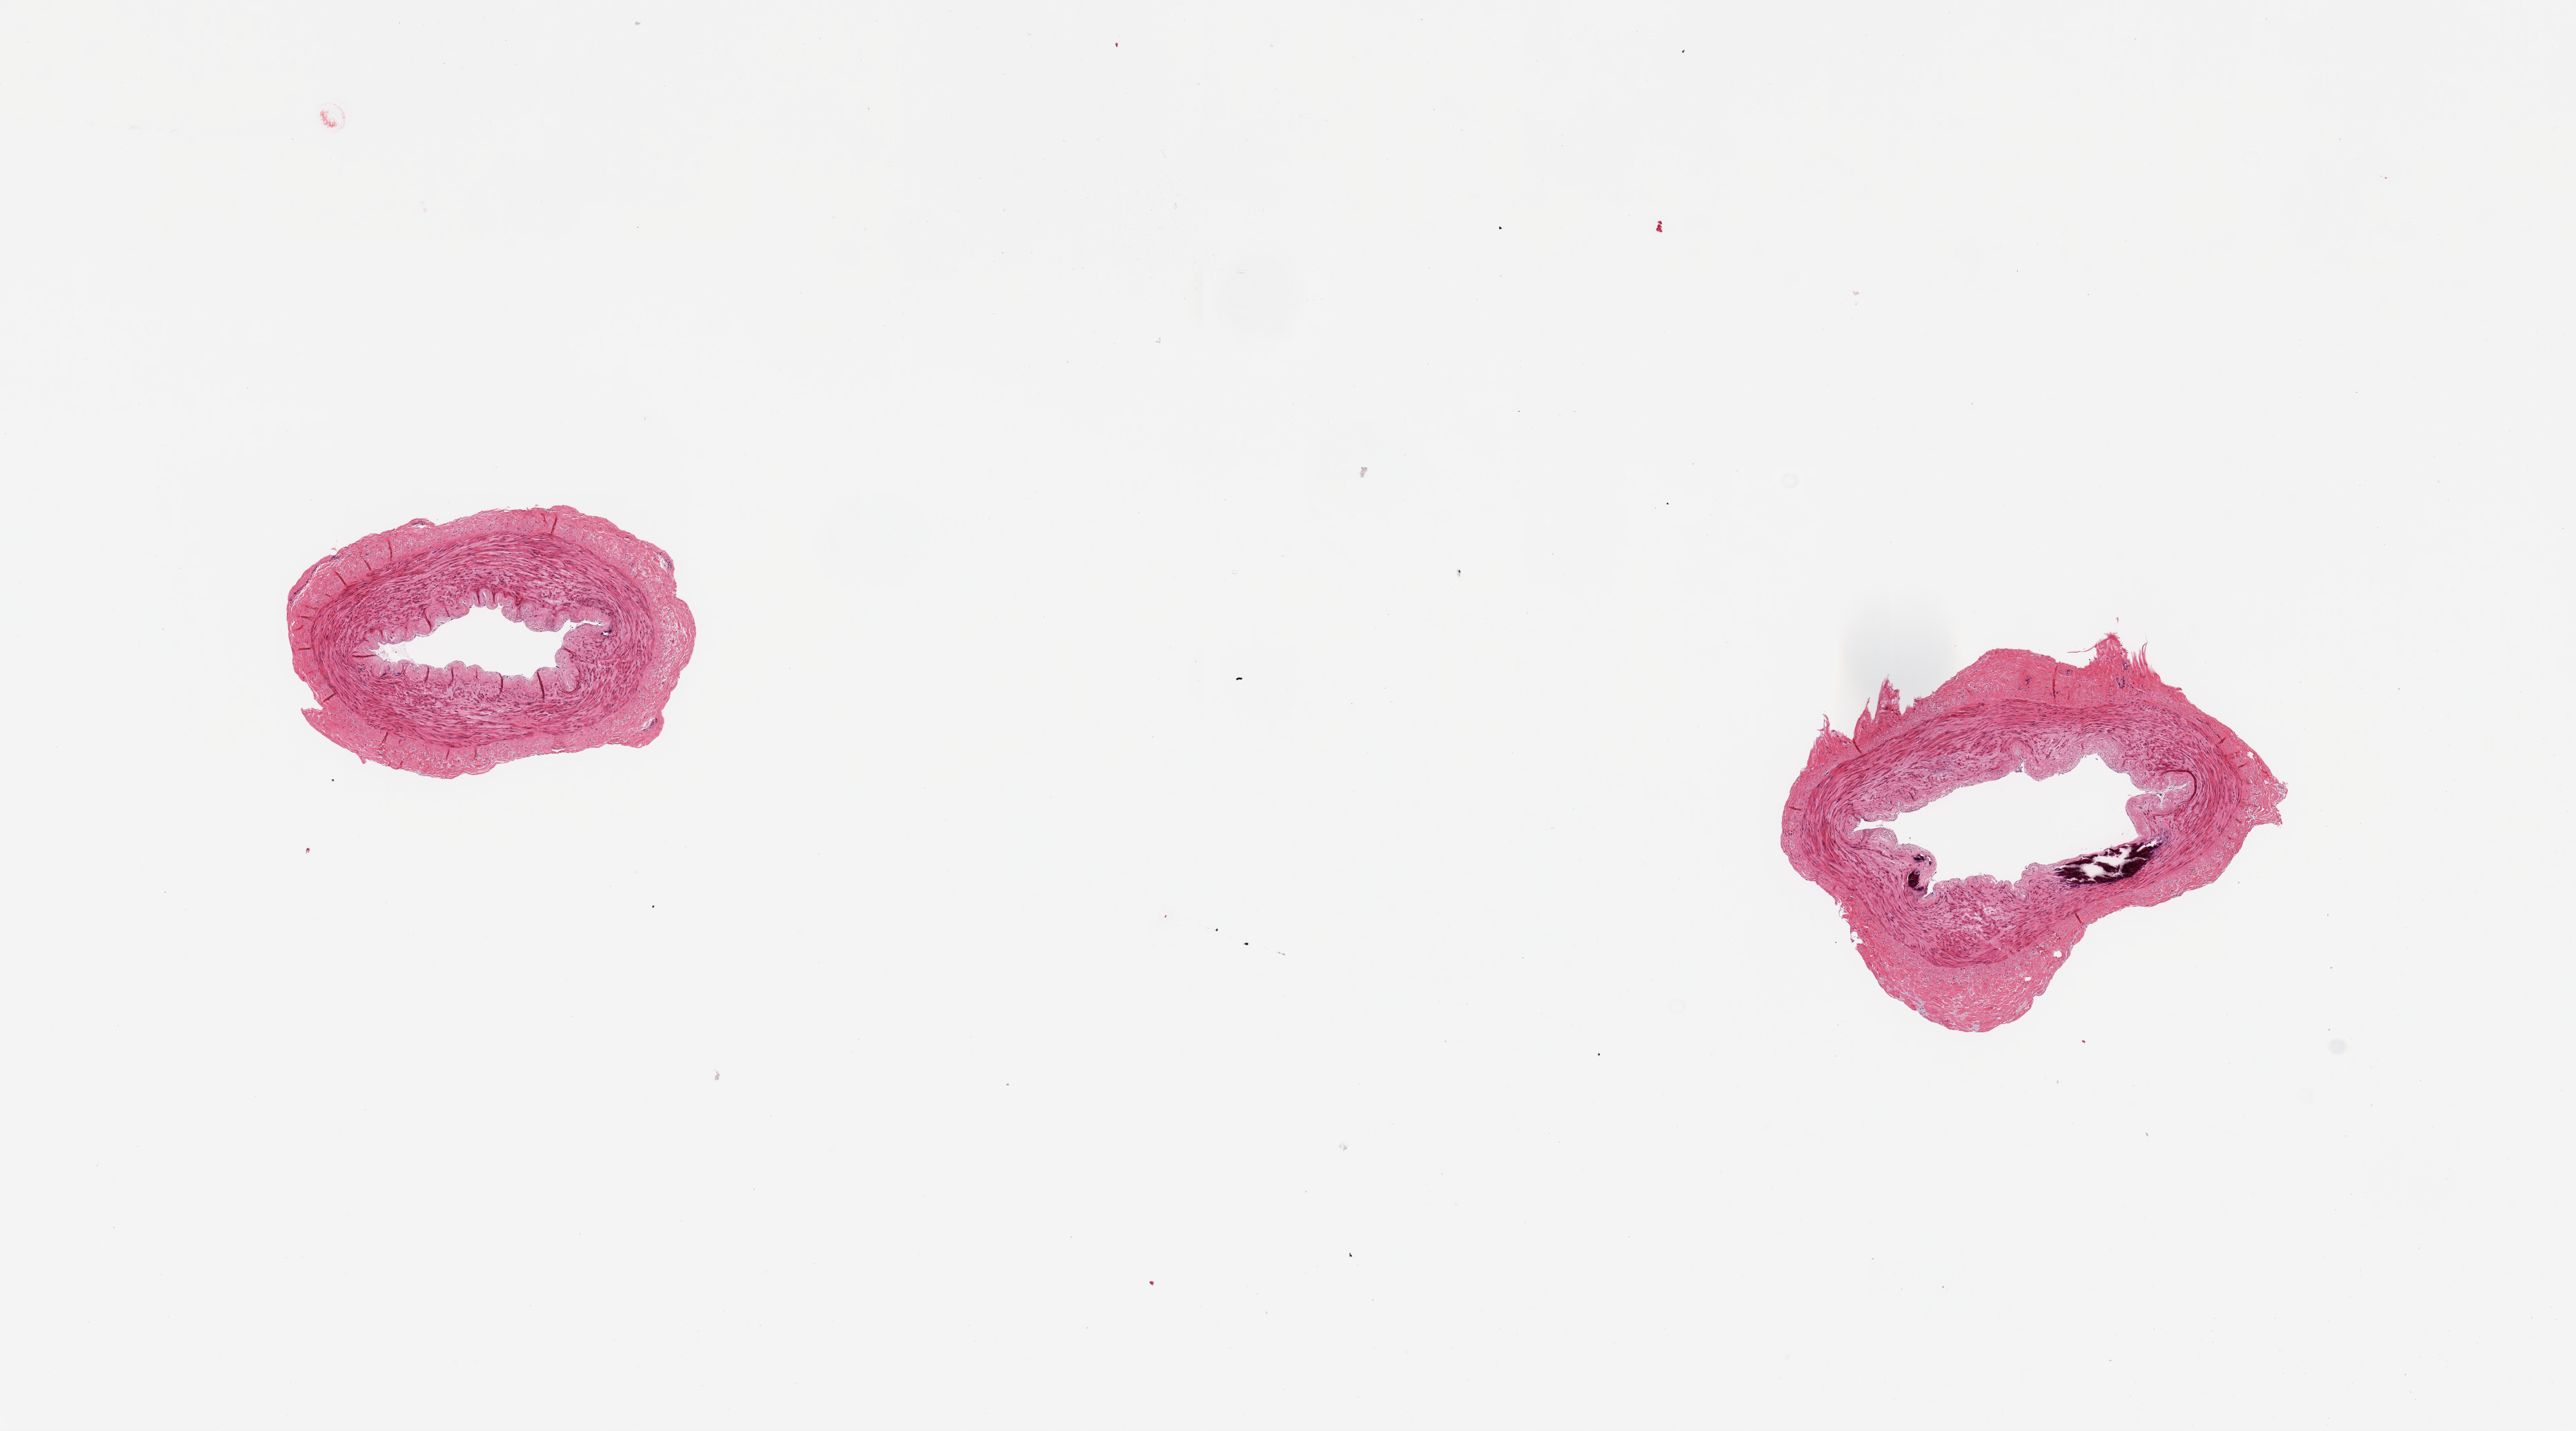
Digitized H&E-stained section — whole scanned area (about 14.8 x 8.2 mm) shown as a low-resolution overview. PAXgene-fixed paraffin-embedded (PFPE) section. Target tissue: tibial artery. Tissue donor sample.
Review note (as recorded): 2 pieces; calcific foci; no plaques; well trimmed.